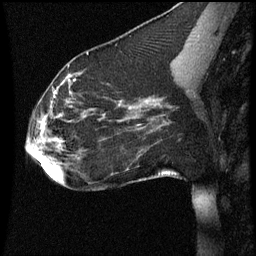
Breast MRI (dynamic contrast-enhanced), one sagittal slice; position 26 of 60 along the scan axis; dynamic contrast-enhanced series, image 2 of 3 at this slice position (ordered by acquisition); 1.5 T; TE 4.2 ms, TR 8.9 ms; 256 × 256 image matrix, field of view 200 × 200 mm. Patient: female, 35 years. Case-level facts recorded for this patient, not image findings: setting: breast cancer imaged before/during neoadjuvant chemotherapy; receptor status: HER2-positive.
Structures marked on this image (semi-automatically segmented with operator editing):
- analysis volume of interest (the breast-tissue region the enhancement analysis was run in; not a lesion): bounding box [x1, y1, x2, y2] px = [24, 66, 177, 177]
- tumour enhancement mask (voxels above the 70 % enhancement threshold inside the analysis volume of interest): [36, 76, 150, 157]